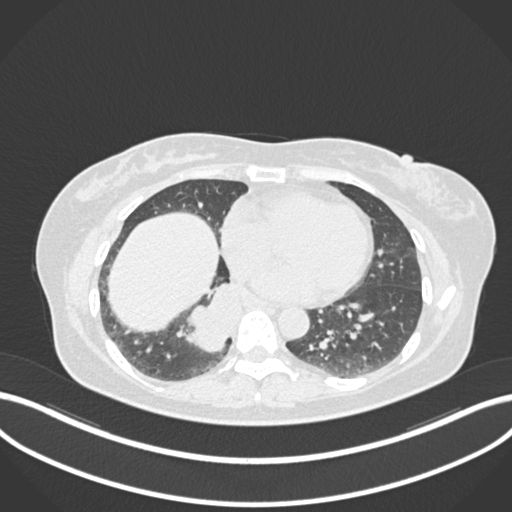
Chest CT, one axial slice. Position 555 of 677 along the scan axis. Reconstruction kernel B30f. 120 kVp. Lung window (W 1500 / L -600 HU). 512 × 512 image matrix, field of view 400 × 400 mm. Patient: female, 54 years. From the clinical record (not read from this slice): clinical TNM (as recorded): T4 N0 M0.
Annotated regions visible in this slice (rectangle marked by the reading radiologist):
- lung tumour (recorded histology: adenocarcinoma): bounding box [x1, y1, x2, y2] px = [178, 282, 244, 350]